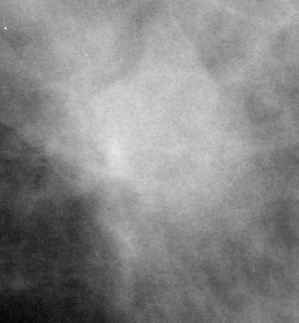
Region of interest cut from a scanned film mammogram (one marked finding); right breast; CC view.
- Finding: mass, shape irregular, margins ill defined / spiculated; BI-RADS assessment category 4; pathology result (as recorded, not read from the image): benign.